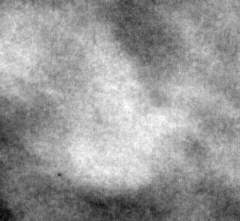
Region of interest cut from a scanned film mammogram (one marked finding); right breast; CC view; BI-RADS breast density category 3 (scale 1–4).
Mass, shape oval, margins ill defined; BI-RADS assessment category 4; subtlety rating 4 on a 1 (subtle) to 5 (obvious) scale; pathology result (as recorded, not read from the image): malignant.